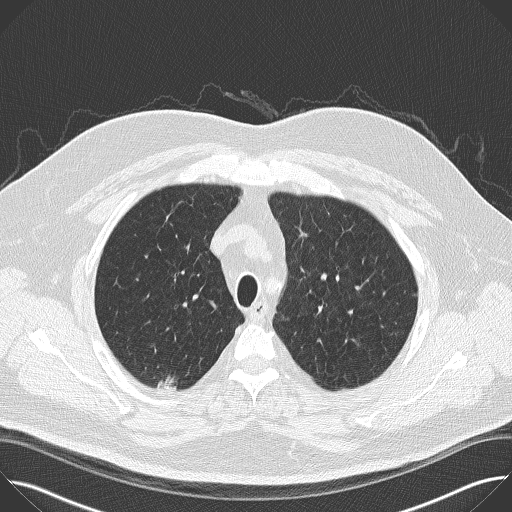
Low-dose screening chest CT, one axial slice. Position 127 of 160 along the scan axis. Reconstruction kernel B50f. Lung window (W 1500 / L -600 HU). 2 mm slice thickness. 512 × 512 image matrix.
Annotated regions visible in this slice (expert manual segmentation):
- lesion 1 (tumor, upper lobe of right lung): bounding box <157,376,177,392> (left, top, right, bottom; pixels)